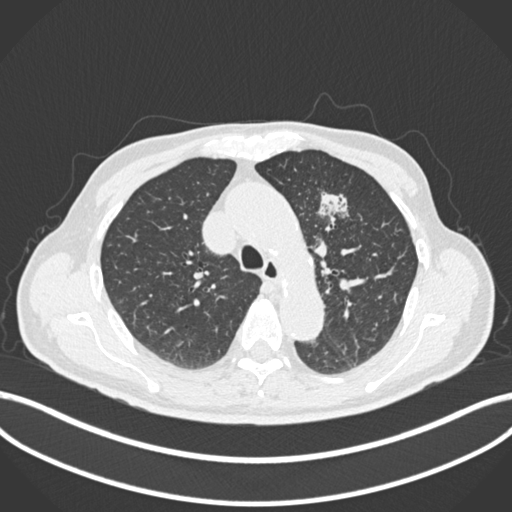
Chest CT, one axial slice. Slice 178 of 261 in the series (ordered by position). Reconstruction kernel B30f. 120 kVp. Lung window (W 1500 / L -600 HU). 512 × 512 image matrix. Patient: male, 74 years. Case-level facts recorded for this patient, not image findings: clinical TNM (as recorded): T2b N0 M1c.
Outlined on this slice (rectangle marked by the reading radiologist):
- lung tumour (recorded histology: adenocarcinoma): bounding box [x1, y1, x2, y2] px = [312, 186, 356, 225]